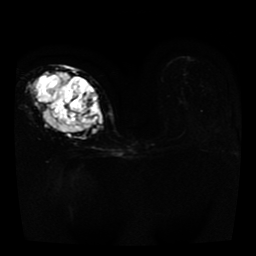
Breast MRI, one axial slice. Position 22 of 41 along the scan axis. Diffusion-weighted series; image 2 of 4 stored at this slice position (different b-values; order by instance number). 1.5 T. 5 mm slice thickness. 256 × 256 image matrix, field of view 330 × 330 mm. Female patient.
Outlined on this slice (manually delineated by an expert):
- tumour on diffusion-weighted imaging: bounding box [x1, y1, x2, y2] px = [36, 73, 103, 130]